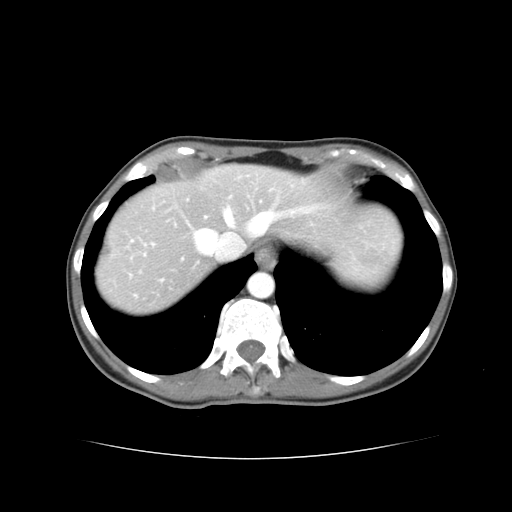
Contrast-enhanced abdominal CT, one axial slice. Slice 33 of 38 in the series (ordered by position). Reconstruction kernel STANDARD. 120 kVp. Soft-tissue window (W 400 / L 40 HU). 512 × 512 image matrix, field of view 340 × 340 mm. Female patient, age 54 years. Case-level facts recorded for this patient, not image findings: diagnosis: colorectal cancer liver metastases, imaged before liver resection; multiple liver metastases: yes; largest metastasis: 1.1 cm; chemotherapy before resection: yes.
Annotated regions visible in this slice (manually delineated by an expert):
- hepatic veins: bounding box [x1, y1, x2, y2] px = [197, 190, 319, 251]
- liver: [97, 166, 399, 311]
- planned liver remnant (the part of the liver to remain after resection): [207, 165, 399, 258]
- portal vein (with intrahepatic branches): [198, 209, 271, 253]
- liver metastasis: [105, 247, 114, 255]